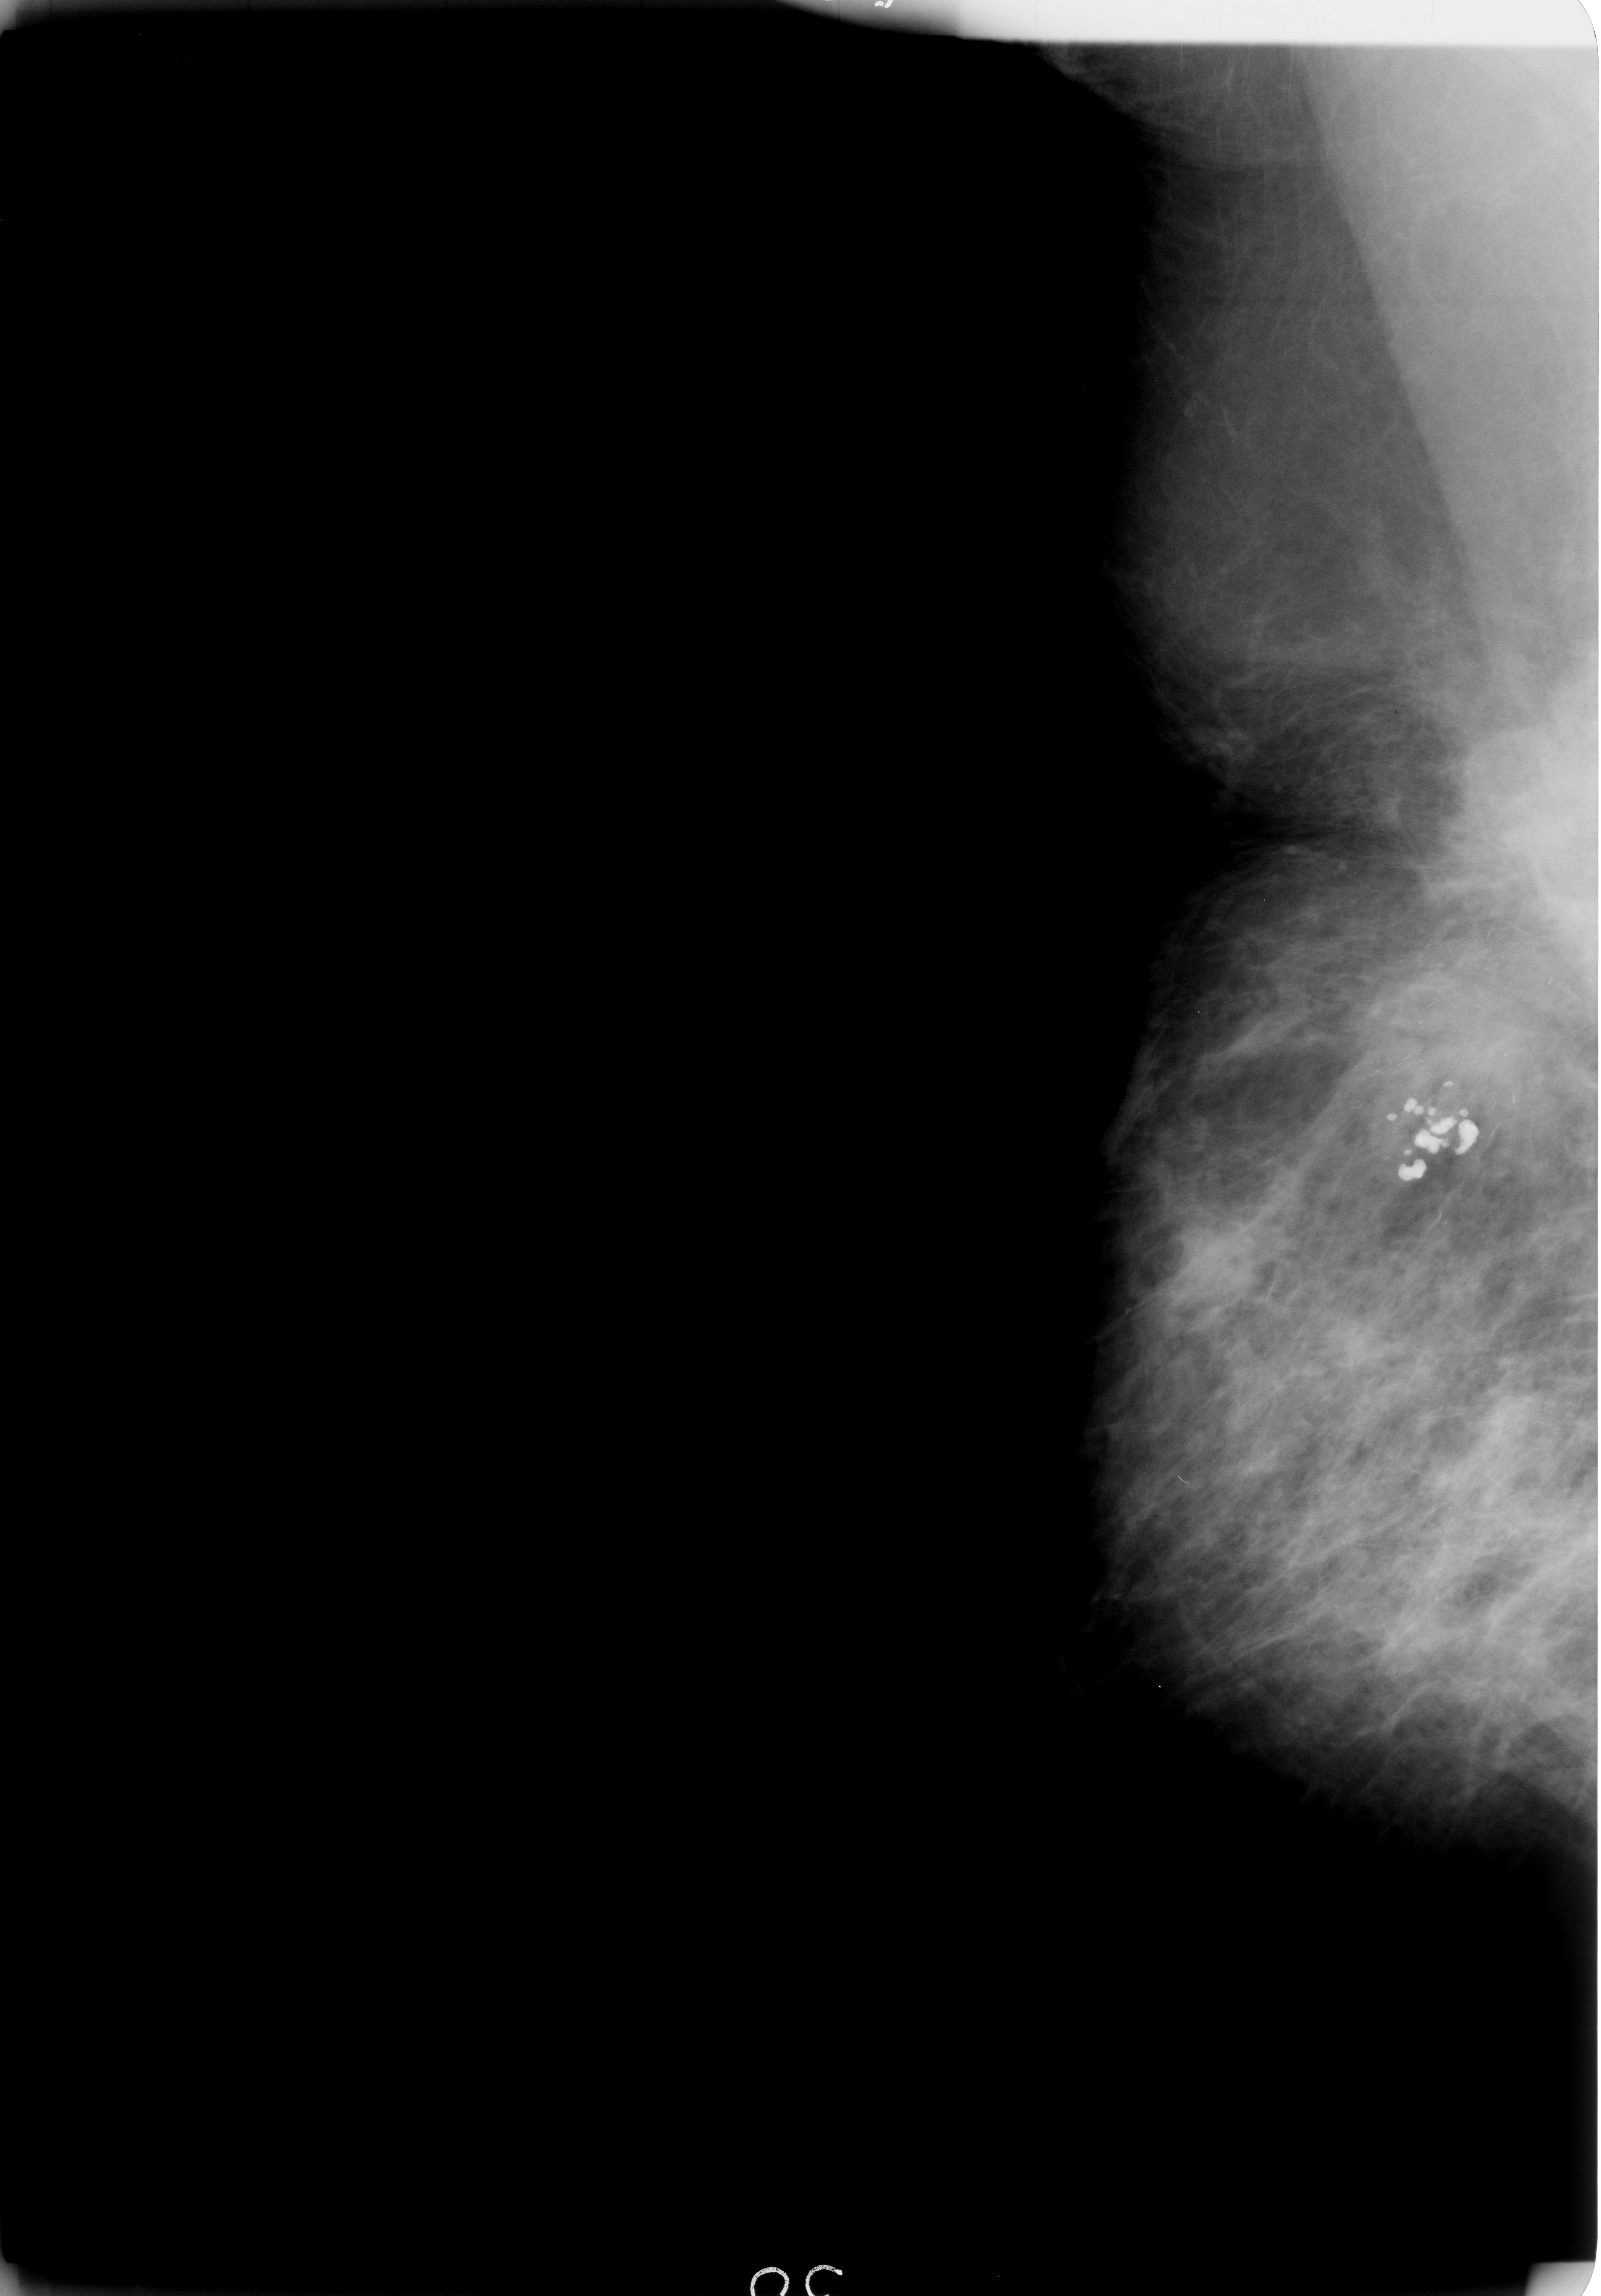
Digitized screen-film mammogram. Right breast. Mediolateral oblique (MLO) view. Breast composition: scattered fibroglandular densities (BI-RADS density category 2 of 4). 1601 × 2296 image matrix.
Marked abnormalities (boxes around the expert regions of interest):
- Finding 1 of 3: calcifications, morphology pleomorphic / fine linear branching, distribution segmental; BI-RADS assessment category 5; pathology (as recorded): malignant: box from (x=1387, y=1039) to (x=1423, y=1078) px
- Finding 2 of 3: calcifications, morphology pleomorphic / fine linear branching, distribution segmental; BI-RADS assessment category 5; pathology result (as recorded, not read from the image): malignant: (x=1472, y=920)–(x=1499, y=953)
- Finding 3 of 3: calcifications, morphology pleomorphic / fine linear branching, distribution segmental; BI-RADS assessment category 5; pathology (as recorded): malignant: (x=1535, y=996)–(x=1561, y=1031)